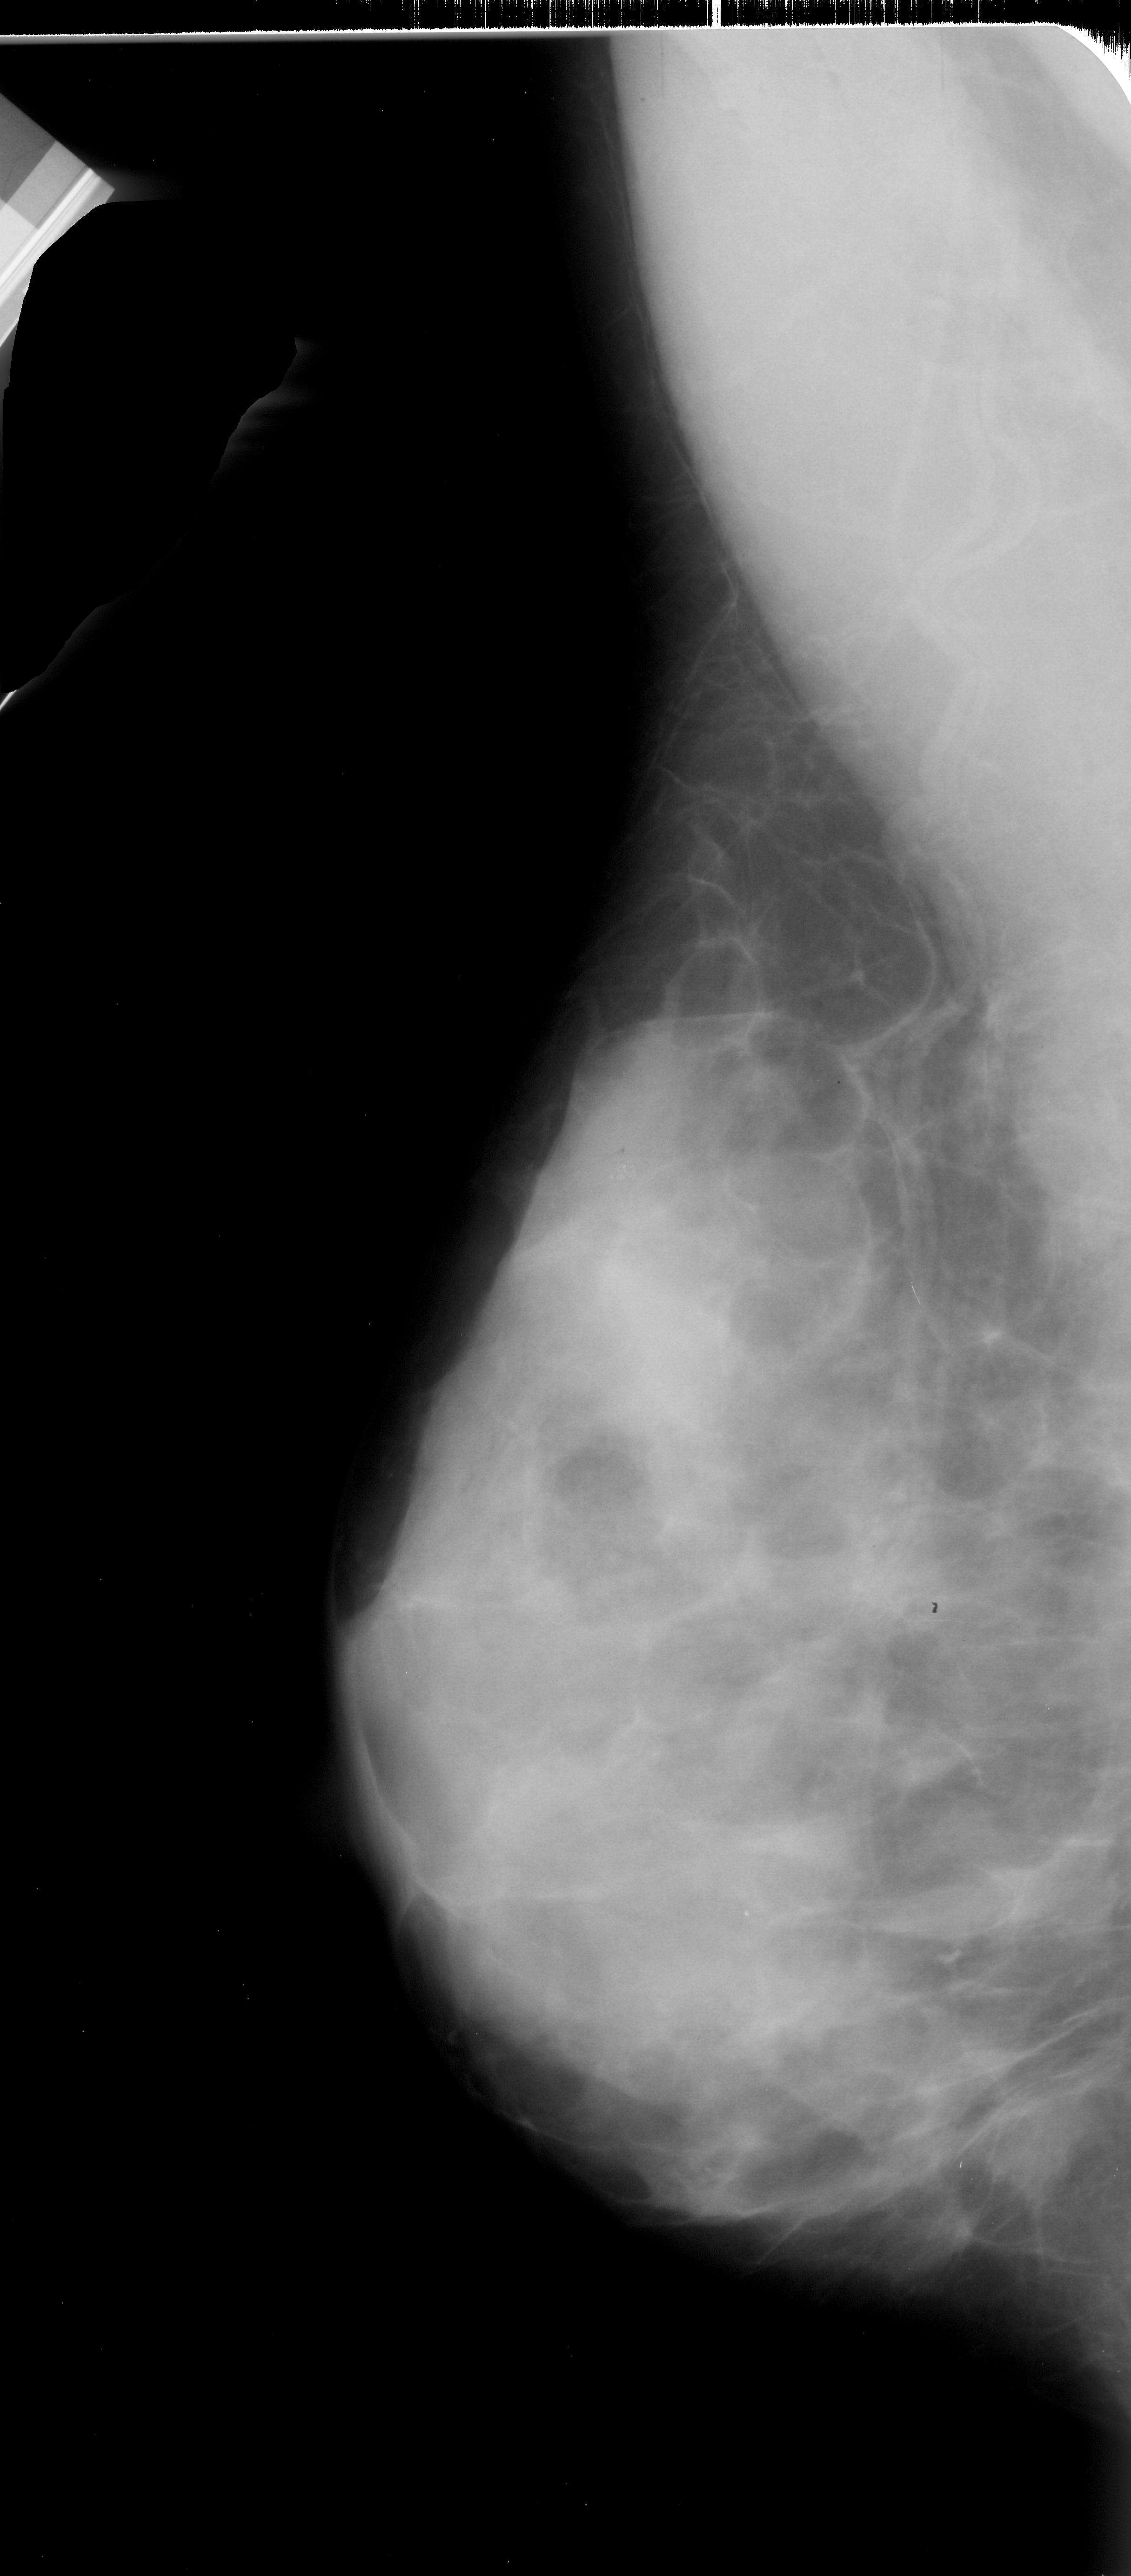
Digitized screen-film mammogram; left breast; MLO view; BI-RADS breast density category 4 (scale 1–4).
- Finding: calcifications, morphology punctate, distribution clustered; BI-RADS assessment category 4; subtlety rating 1 on a 1 (subtle) to 5 (obvious) scale; pathology (as recorded): malignant.